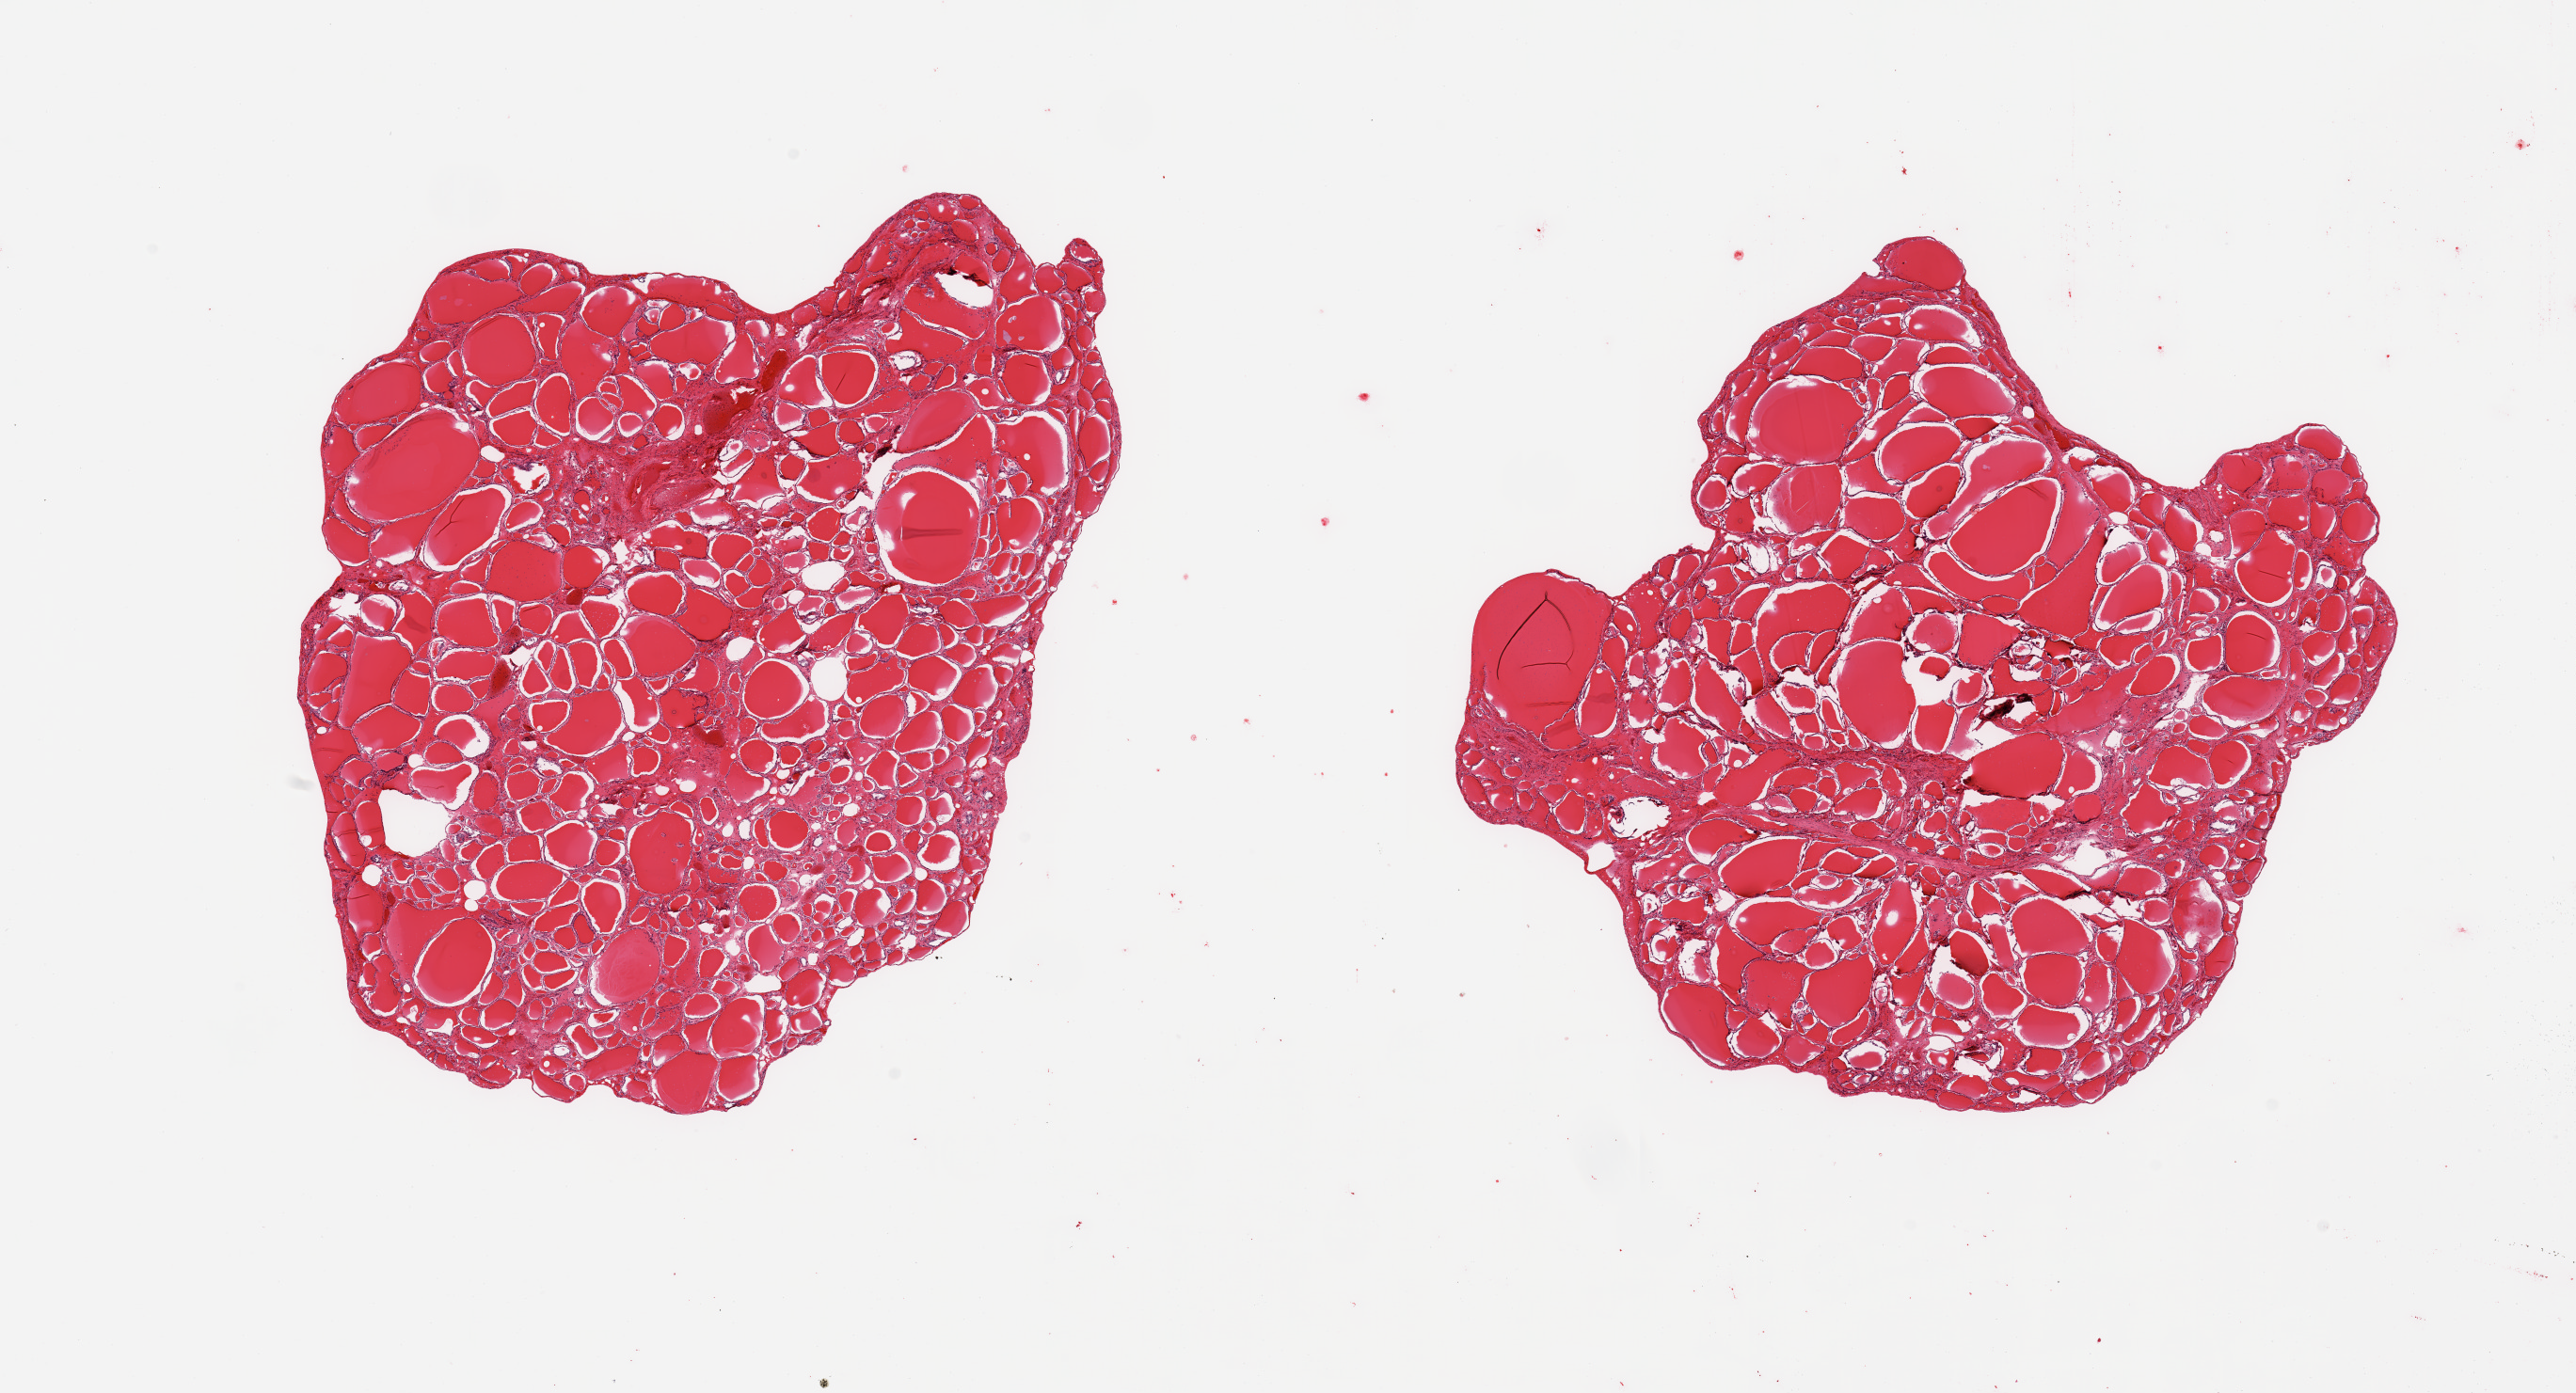
Digitized H&E-stained section, brightfield, low-resolution overview of the scanned area, about 21.7 x 11.7 mm. PAXgene-fixed paraffin-embedded (PFPE) section. Section of thyroid (target tissue). Donor tissue sample. Donor: female.
• pathologist's review note for this sample: 2 pieces; no lesions